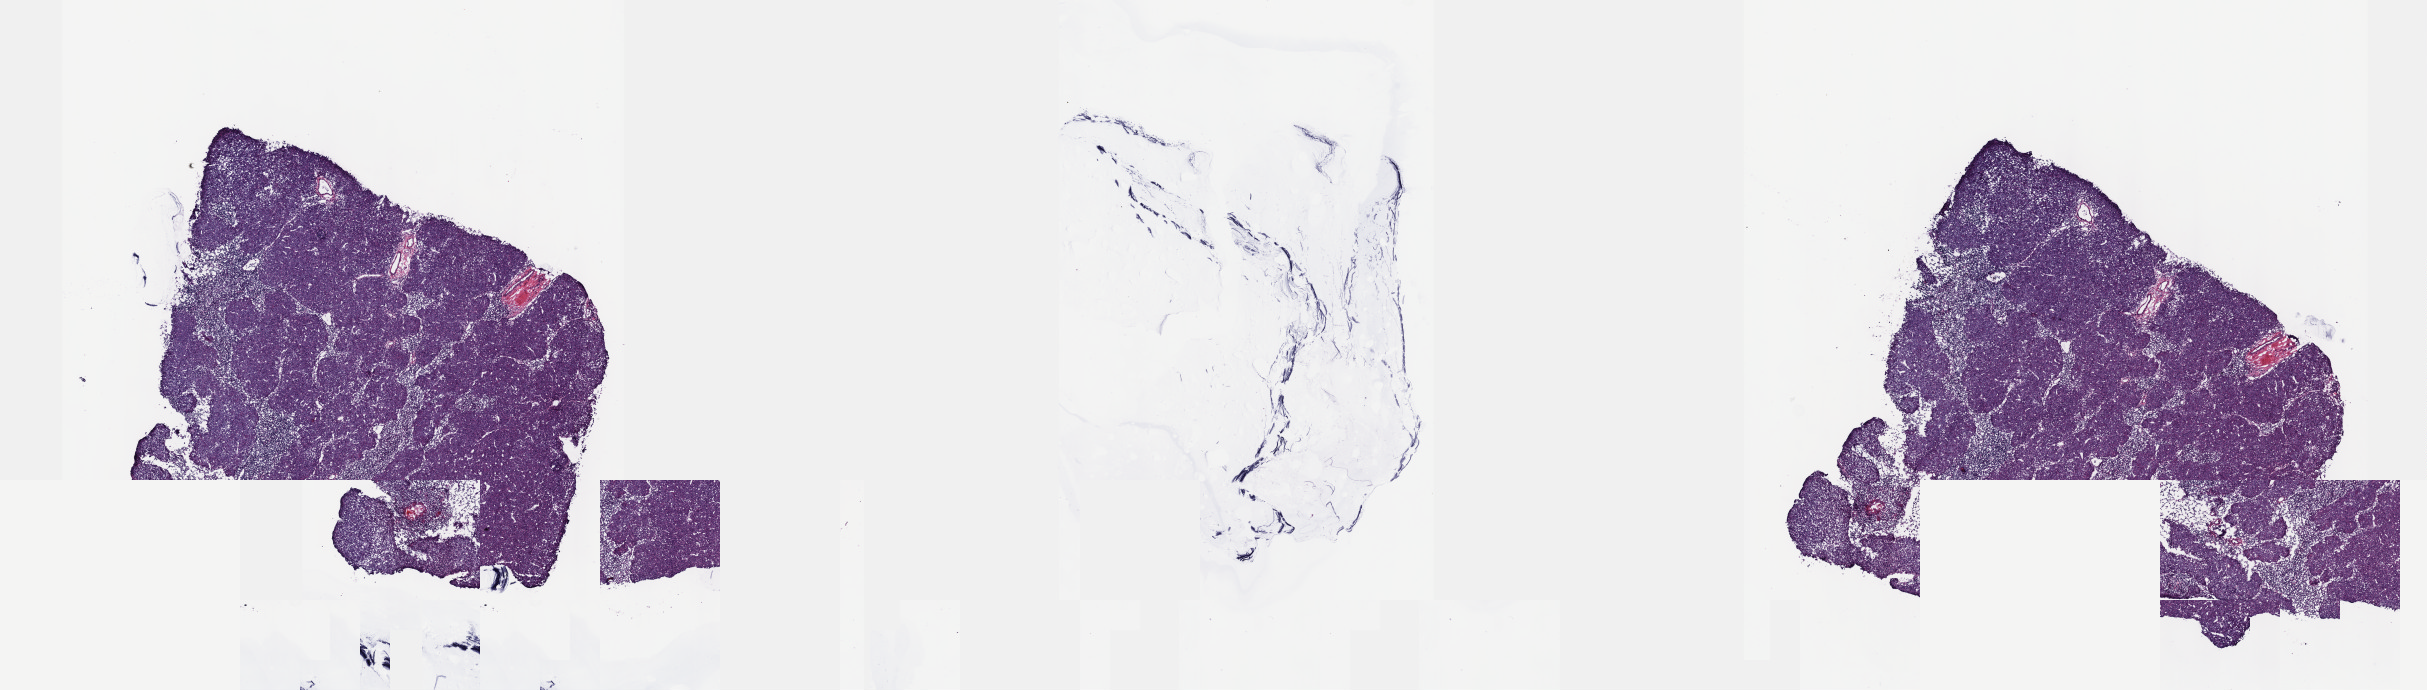
Whole-slide histology image, H&E — shown as a low-resolution overview of the whole scanned area (about 19.6 x 5.6 mm, from a 40x scan); frozen section from the top of the tissue portion; thymus, primary tumour sample. Female patient; age at initial diagnosis 65 years. Slide review estimates, as recorded: tumour cells 100%, tumour nuclei 80%, normal cells 0%, stromal cells 0%, necrosis 0%. Inflammatory infiltration, as recorded: lymphocyte infiltration 2%, monocyte infiltration 0%, neutrophil infiltration 0%.
Diagnosis: Thymoma, type B3, malignant.